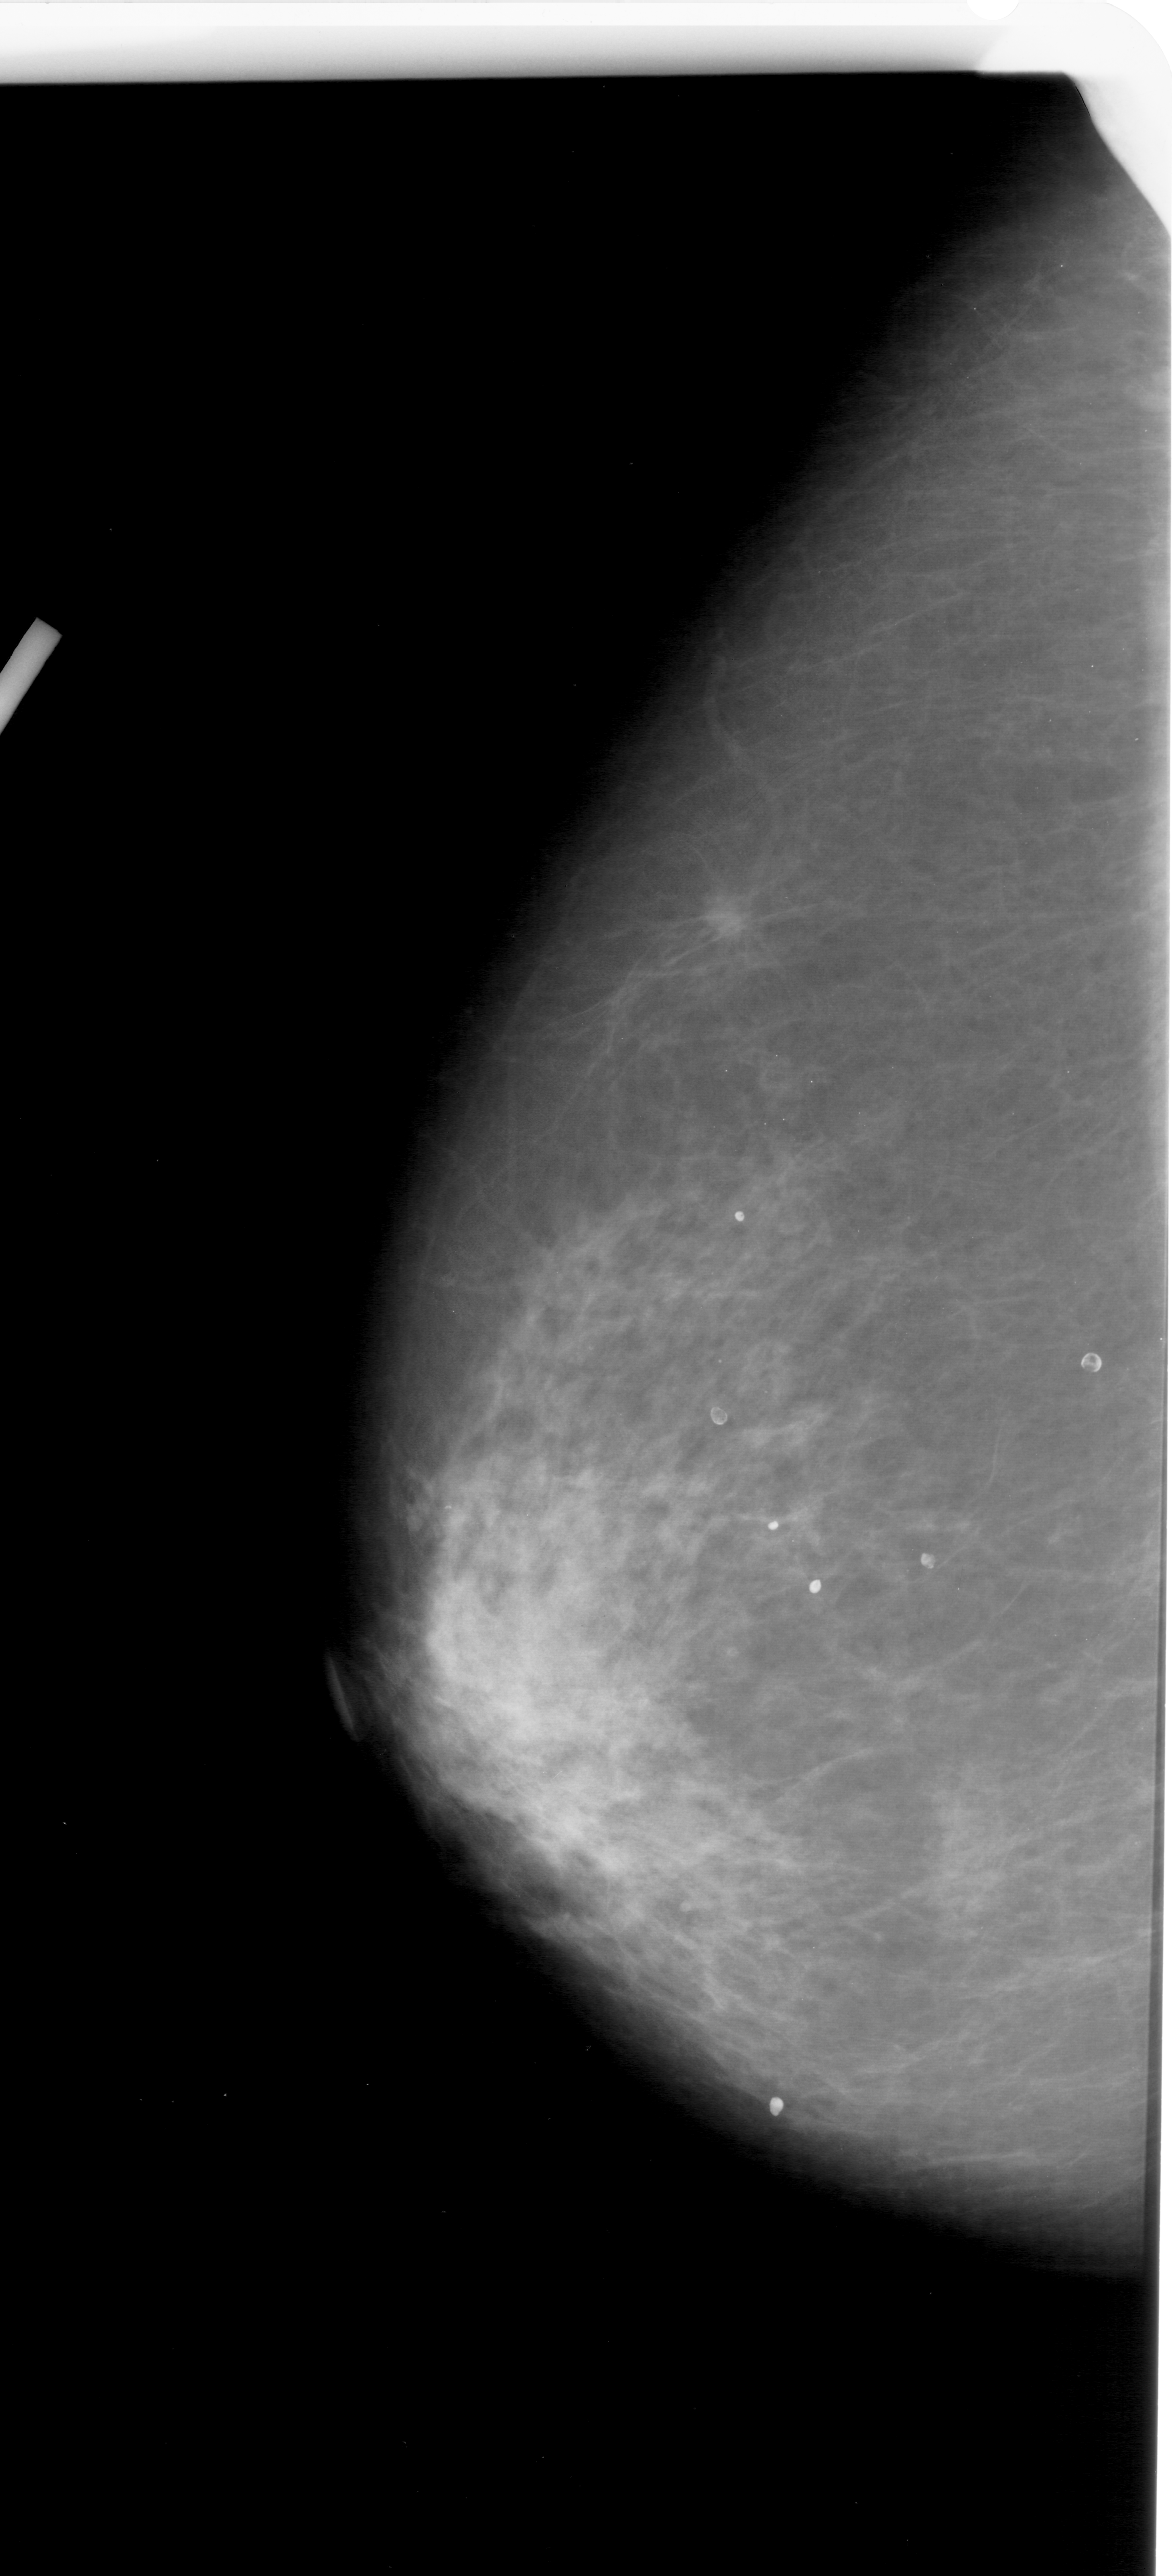
Digitized screen-film mammogram; left breast; craniocaudal (CC) view; BI-RADS breast density category 3 (scale 1–4); 1174 × 2576 image matrix.
Expert-marked regions of interest on this film, with their recorded descriptors:
- mass, shape oval, margins ill defined; BI-RADS assessment category 4; subtlety rating 2 on a 1 (subtle) to 5 (obvious) scale; pathology result (as recorded, not read from the image): malignant: bounding box (x1, y1, x2, y2) in pixels: (684, 884, 770, 947)